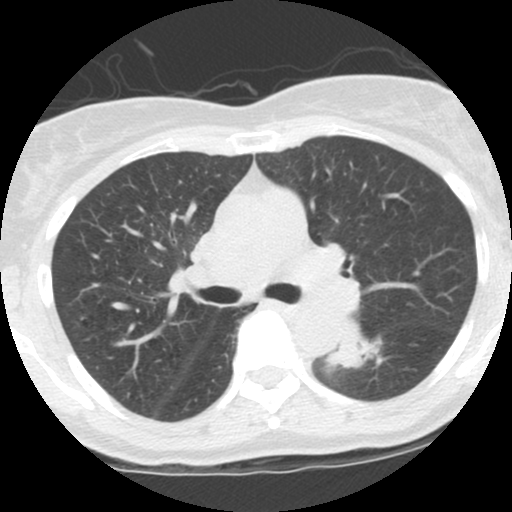
Low-dose screening chest CT, one axial slice; position 69 of 115 along the scan axis; 120 kVp; lung window (W 1500 / L -600 HU); 2.5 mm slice thickness; 512 × 512 image matrix, field of view 290 × 290 mm.
Structures marked on this image (manually delineated by an expert):
- lesion 1 (tumor, lower lobe of left lung): box from (x=326, y=322) to (x=380, y=367) px